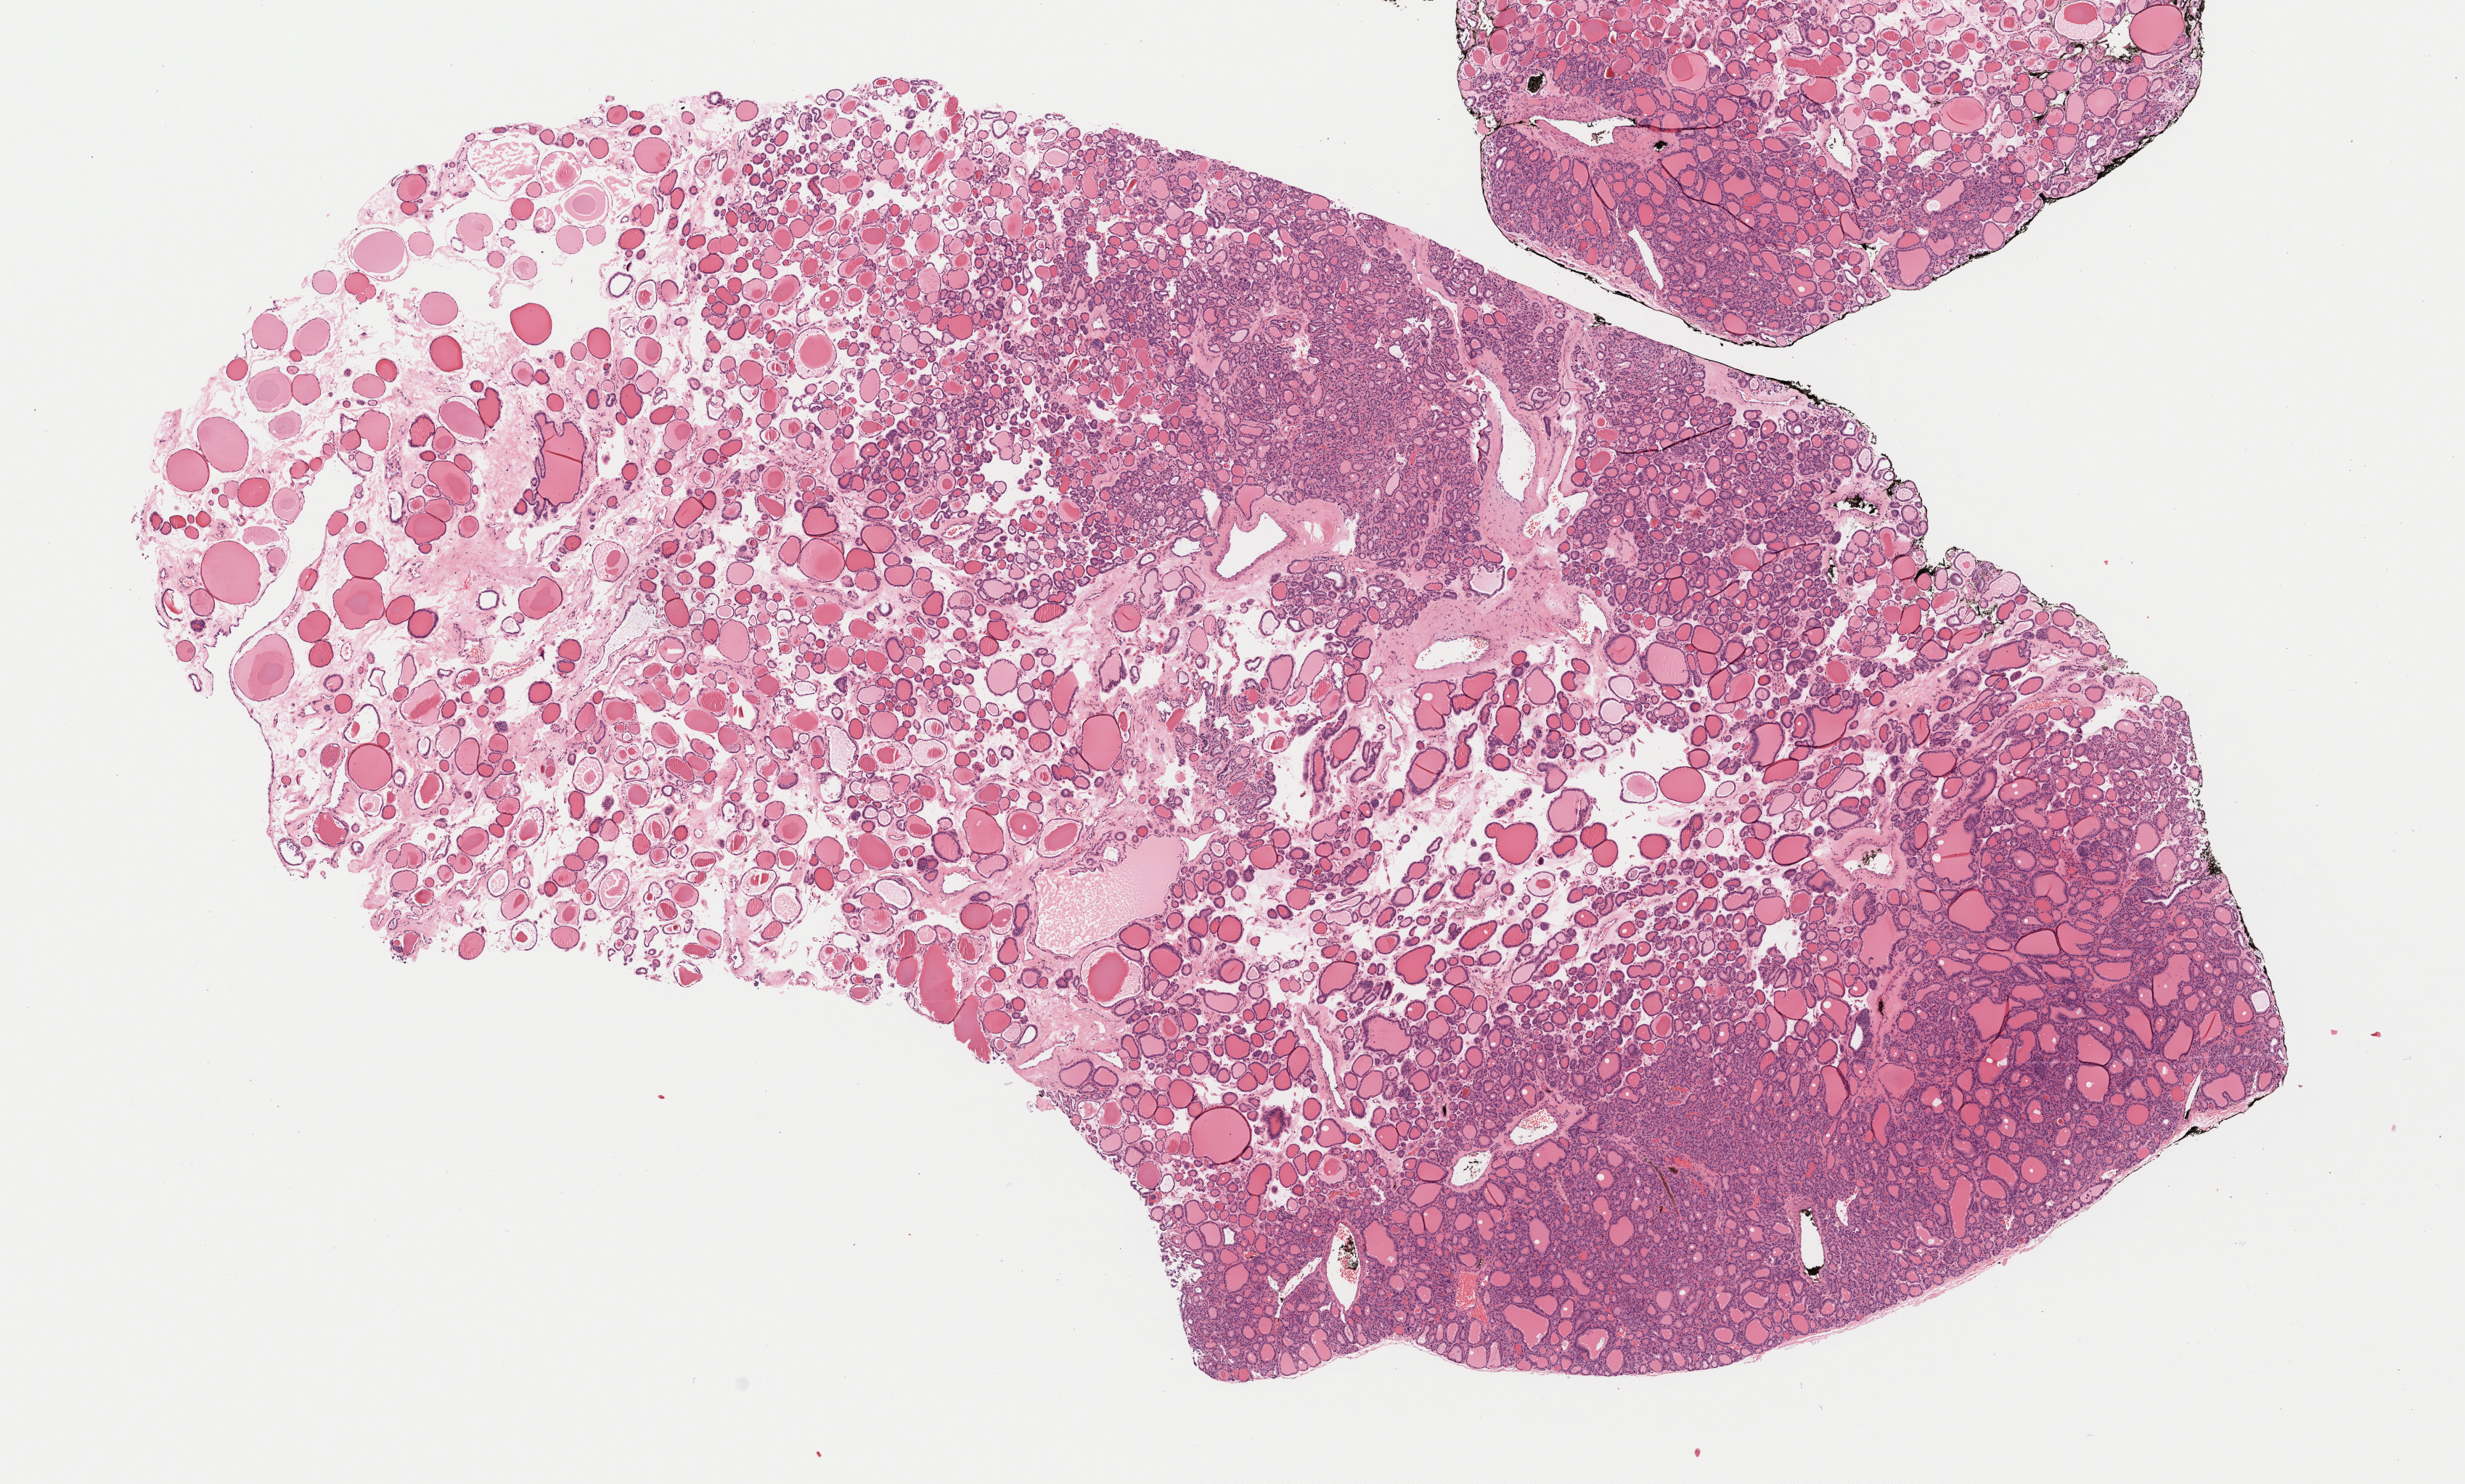
Digitized H&E-stained tissue section (whole slide), low-resolution overview of the scanned area, about 13.7 x 8.2 mm (slide scanned at 40x); formalin-fixed paraffin-embedded (FFPE) diagnostic section; thyroid, primary tumour sample. Male, age 69 years at initial diagnosis.
* pathologic diagnosis: Papillary carcinoma, follicular variant (thyroid gland)
* AJCC pathologic stage: III (7th edition)